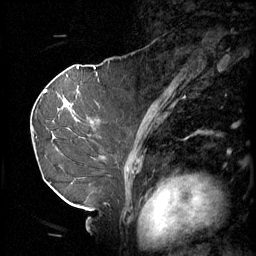
Breast MRI (dynamic contrast-enhanced), one sagittal slice; slice 34 of 60 in the series (ordered by position); 3 images stored at this slice position (order not interpretable as contrast timing); 1.5 T; TE 4.2 ms, TR 11 ms; 256 × 256 image matrix, field of view 220 × 220 mm. Female patient, age 69 years.
Outlined on this slice (semi-automatic segmentation, software-assisted and operator-edited):
- analysis volume of interest (the breast-tissue region the enhancement analysis was run in; not a lesion): bounding box (x1, y1, x2, y2) in pixels: (36, 88, 107, 189)
- tumour enhancement mask (voxels above the 70 % enhancement threshold inside the analysis volume of interest): (64, 100, 76, 121)